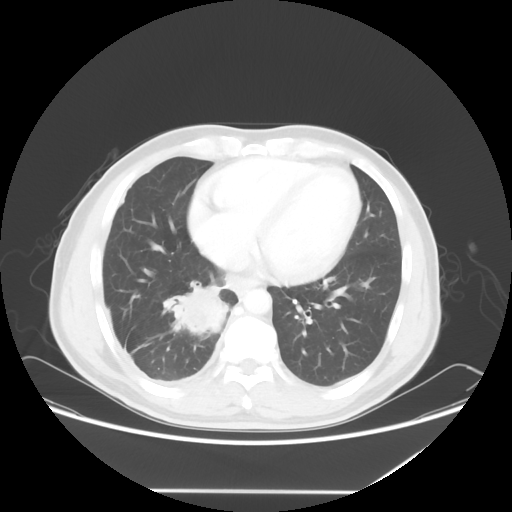
Chest CT, one axial slice; slice 22 of 60 in the series (ordered by position); 120 kVp; lung window (W 1500 / L -600 HU); 5 mm slice thickness; 512 × 512 image matrix, field of view 419 × 419 mm. Male patient, age 48 years. Case-level facts recorded for this patient, not image findings: clinical TNM (as recorded): T3 N3 M1a.
Structures marked on this image (rectangle marked by the reading radiologist):
- lung tumour (recorded histology: squamous cell carcinoma): bounding box <160,277,233,337> (left, top, right, bottom; pixels)